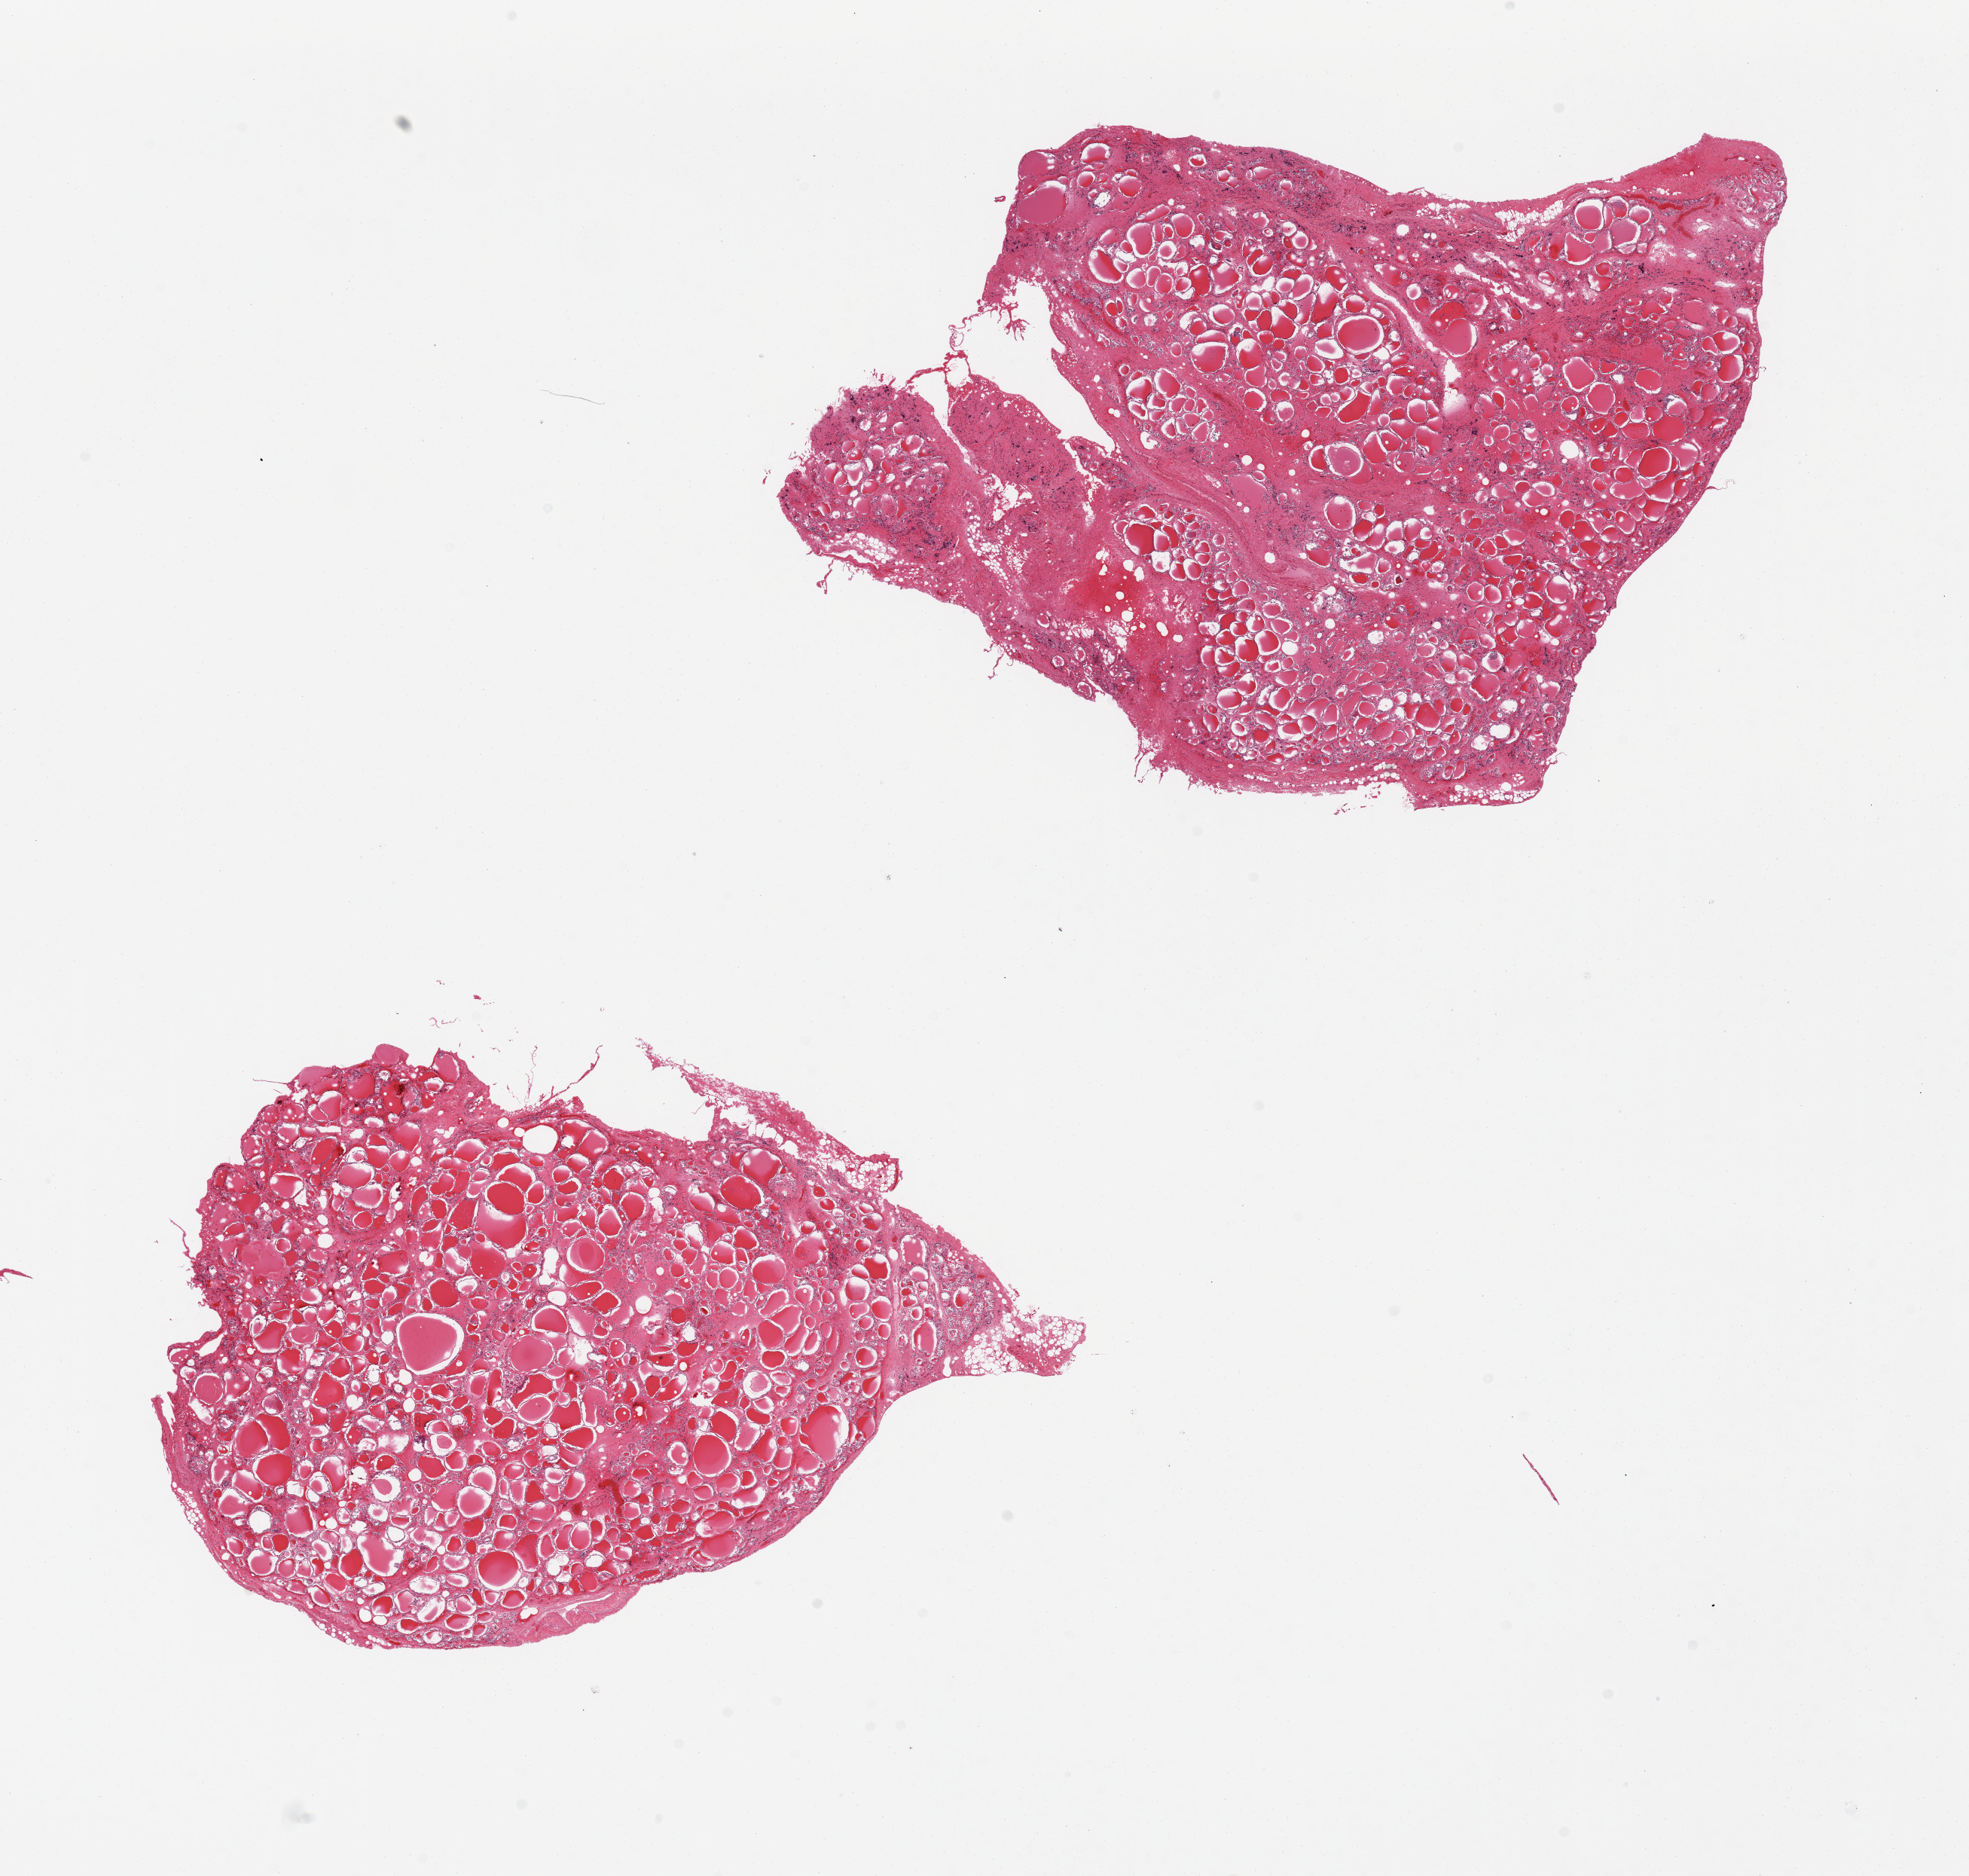
Whole-slide image, haematoxylin and eosin stain, brightfield, low-resolution overview of the scanned area, about 20.7 x 19.7 mm (from a 20x scan). PAXgene-fixed, paraffin-embedded tissue. Sampled site (target tissue): thyroid. Tissue donor sample. Donor sex: female.
• pathologist's review note for this sample: 2 pieces